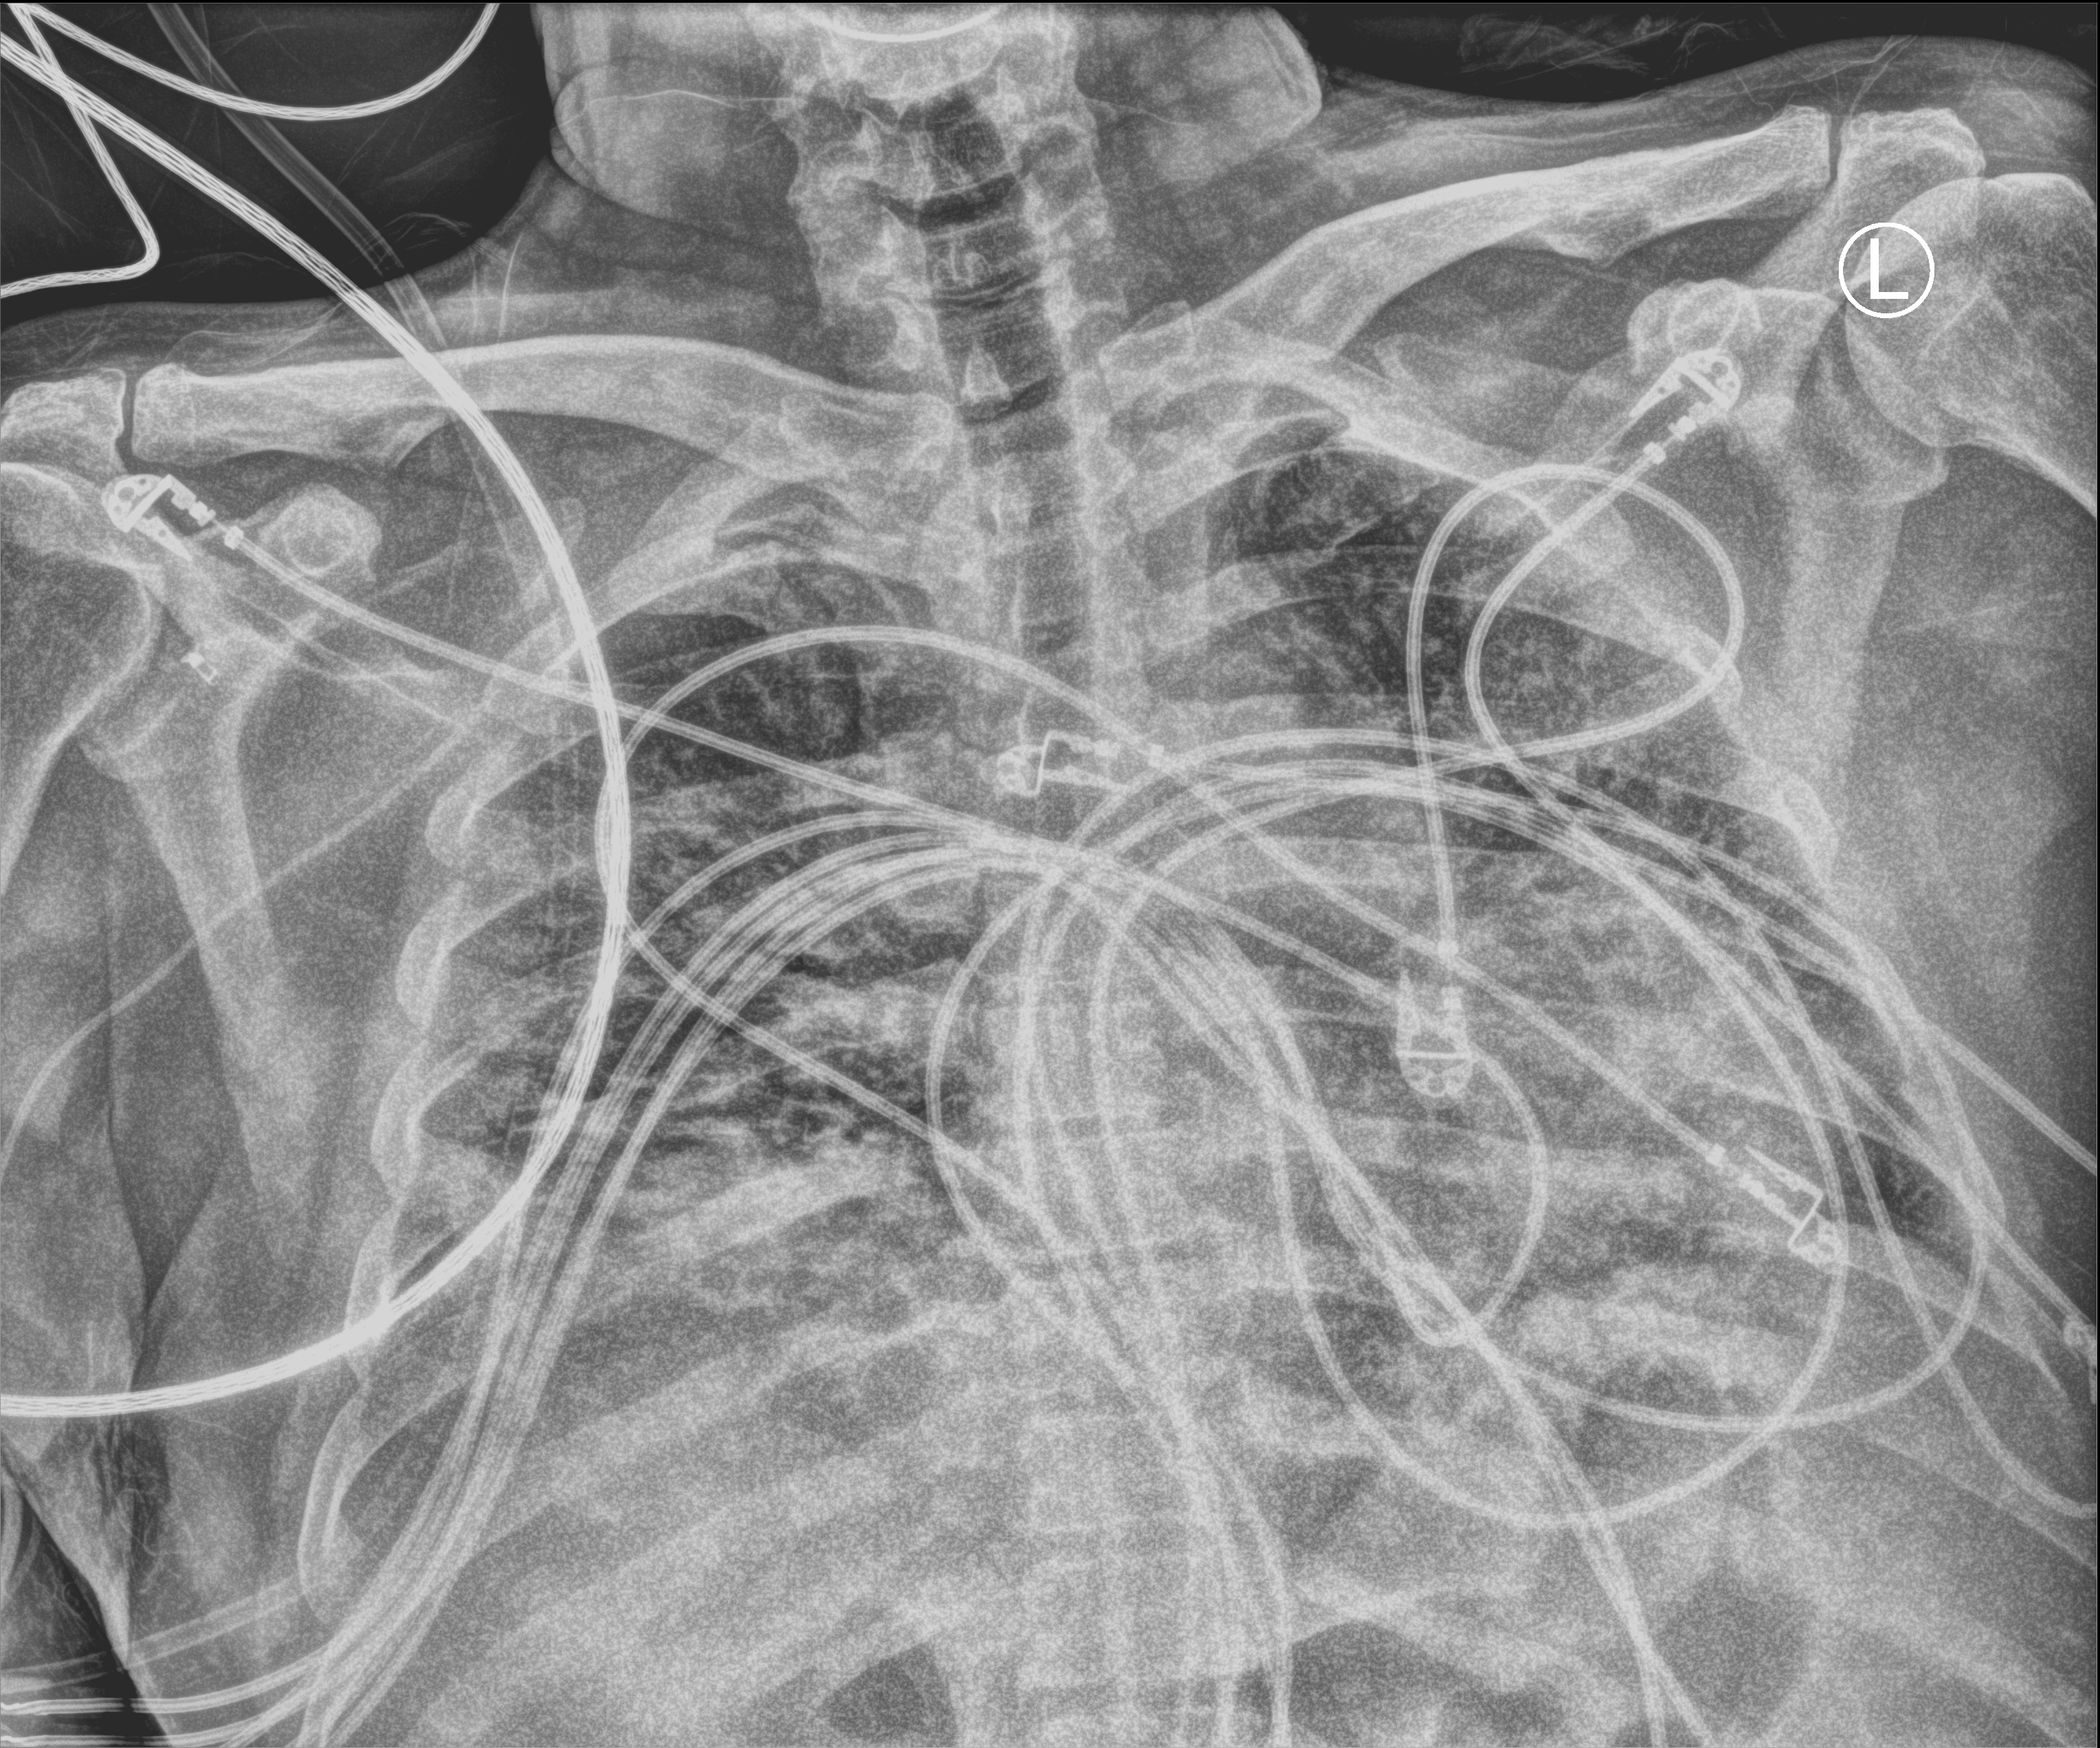
Bedside chest radiograph (computed radiography); anteroposterior (AP) projection. Male patient hospitalised with COVID-19, age 18–59 years.
Admission-level facts for this patient (not findings on this image; timing relative to this image not recorded): other chronic lung disease (admission record): no.